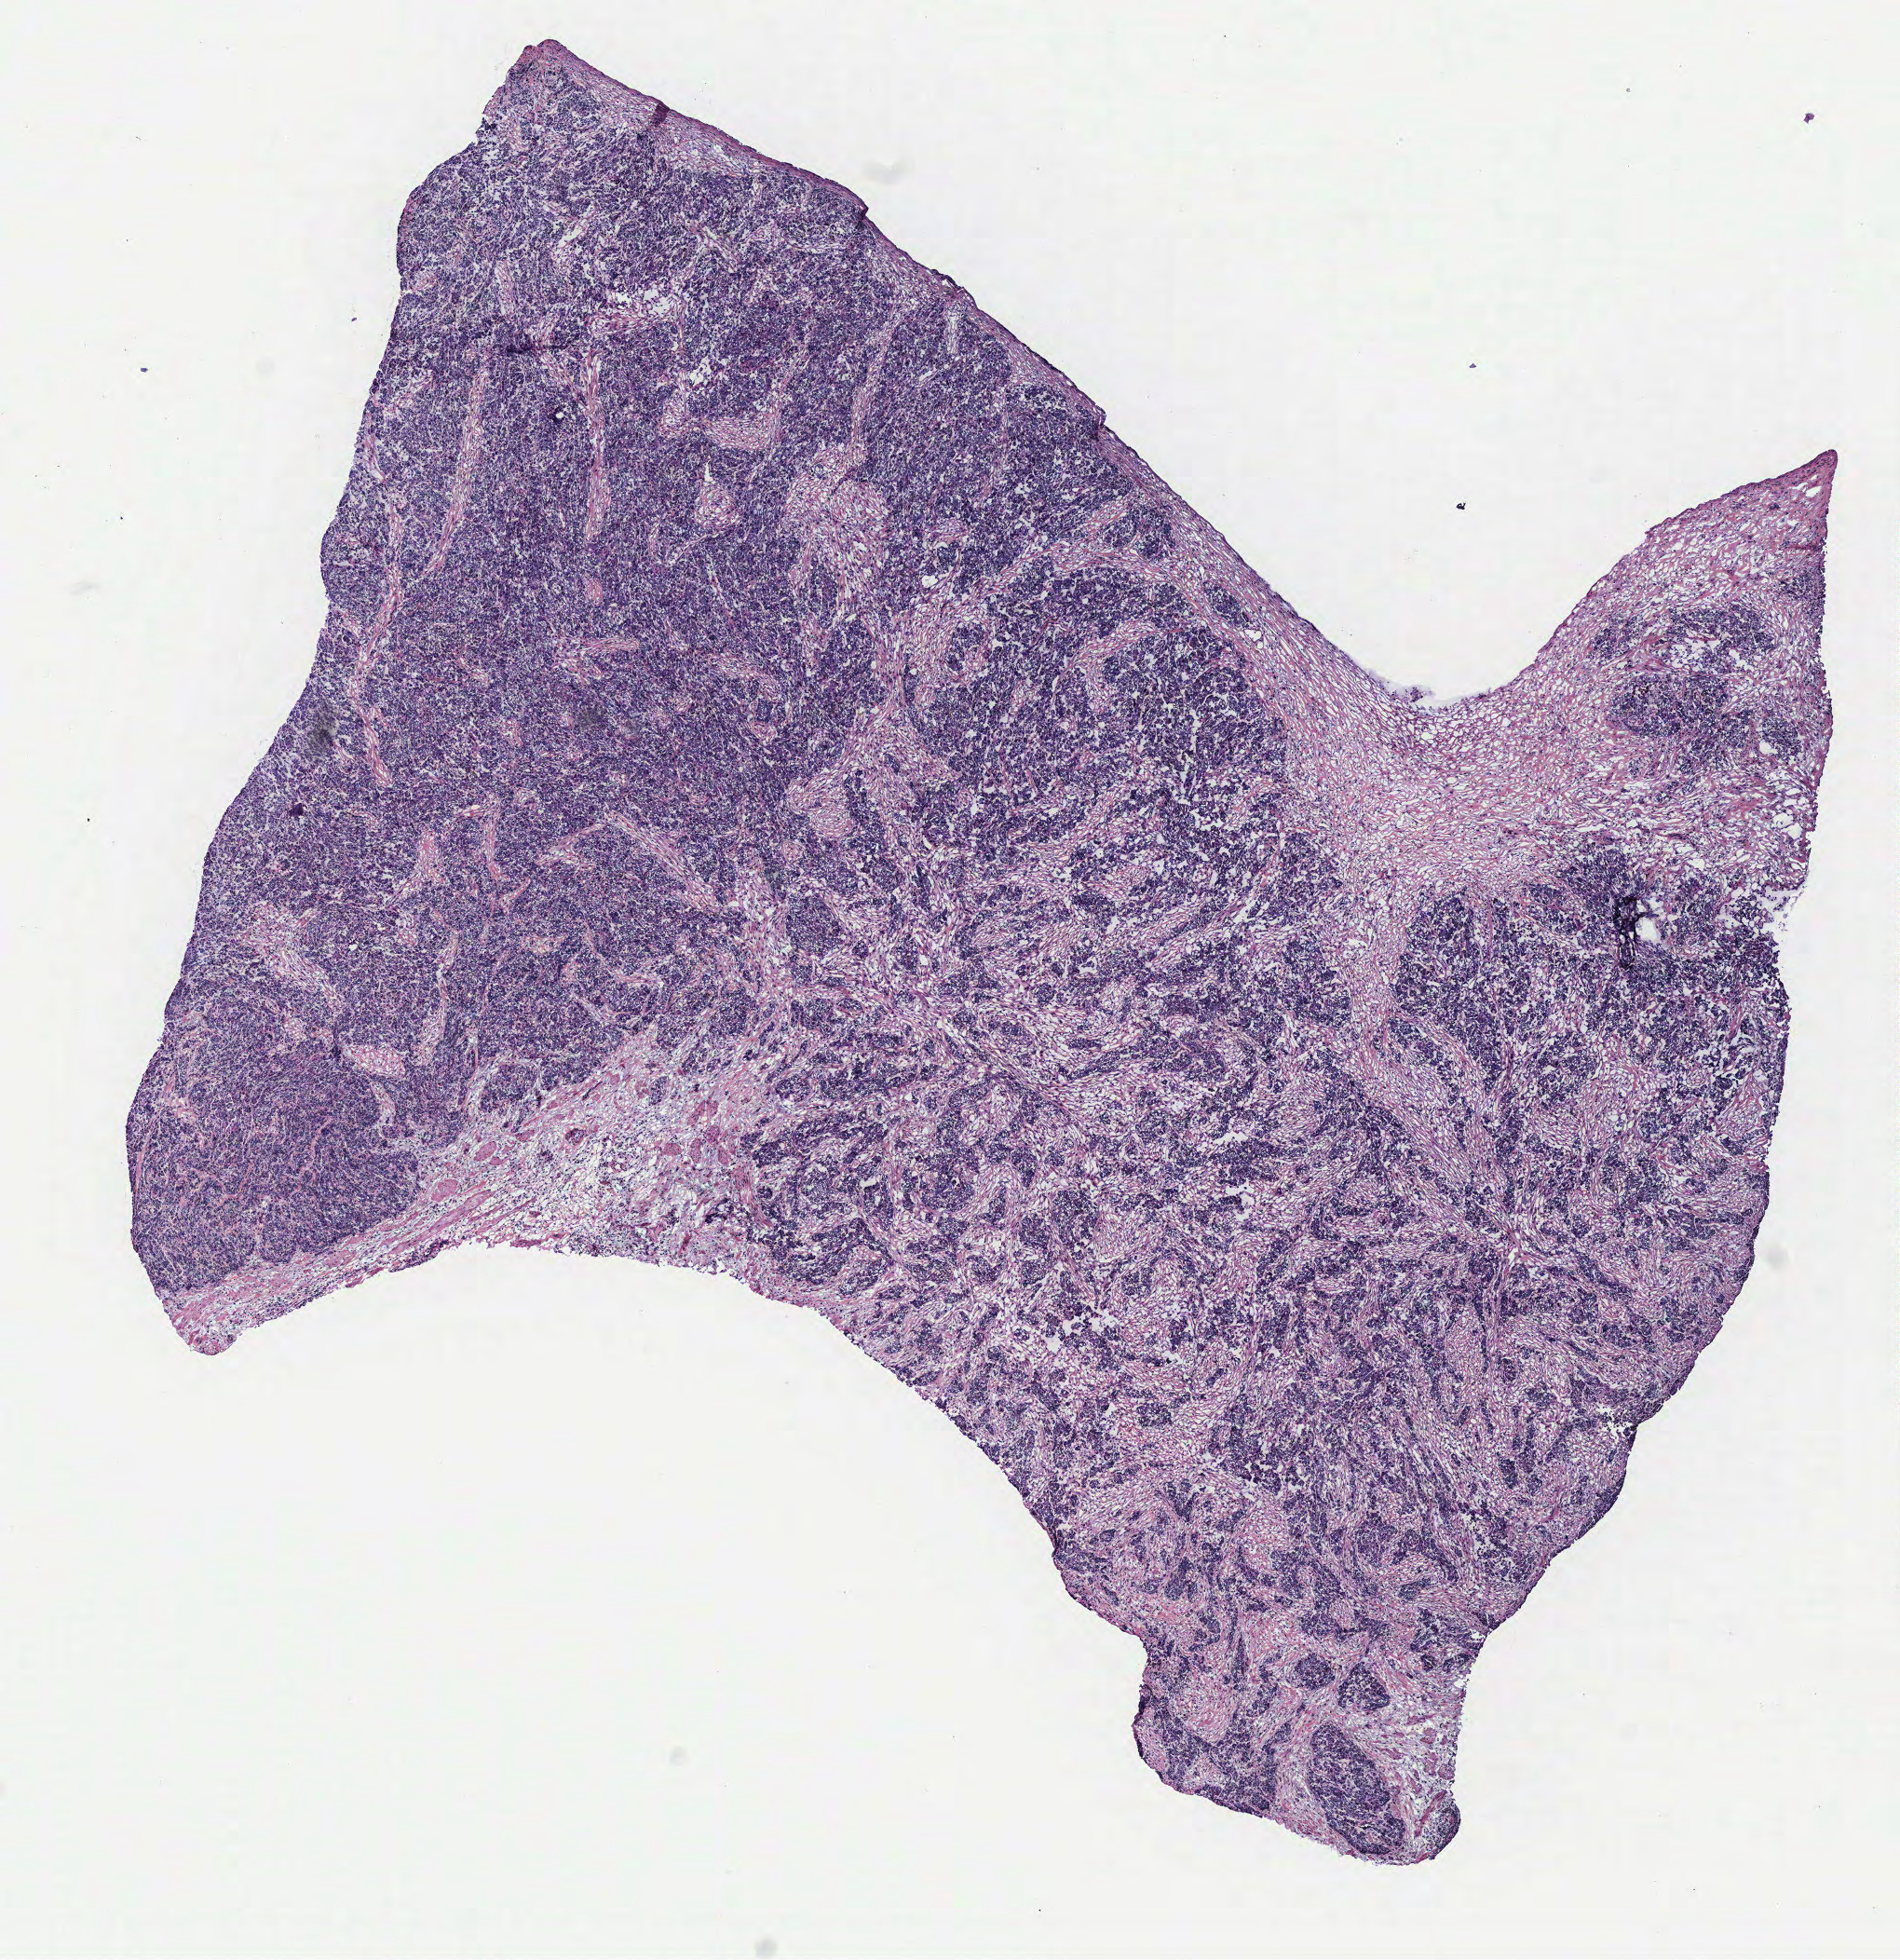
H&E-stained whole-slide image — shown as a low-resolution overview of the whole scanned area (about 8.2 x 8.4 mm). Ovary, tumour tissue. Female, 77 y/o.
* primary tumour site (as recorded): ovary
* histologic diagnosis: Serous adenocarcinoma, NOS